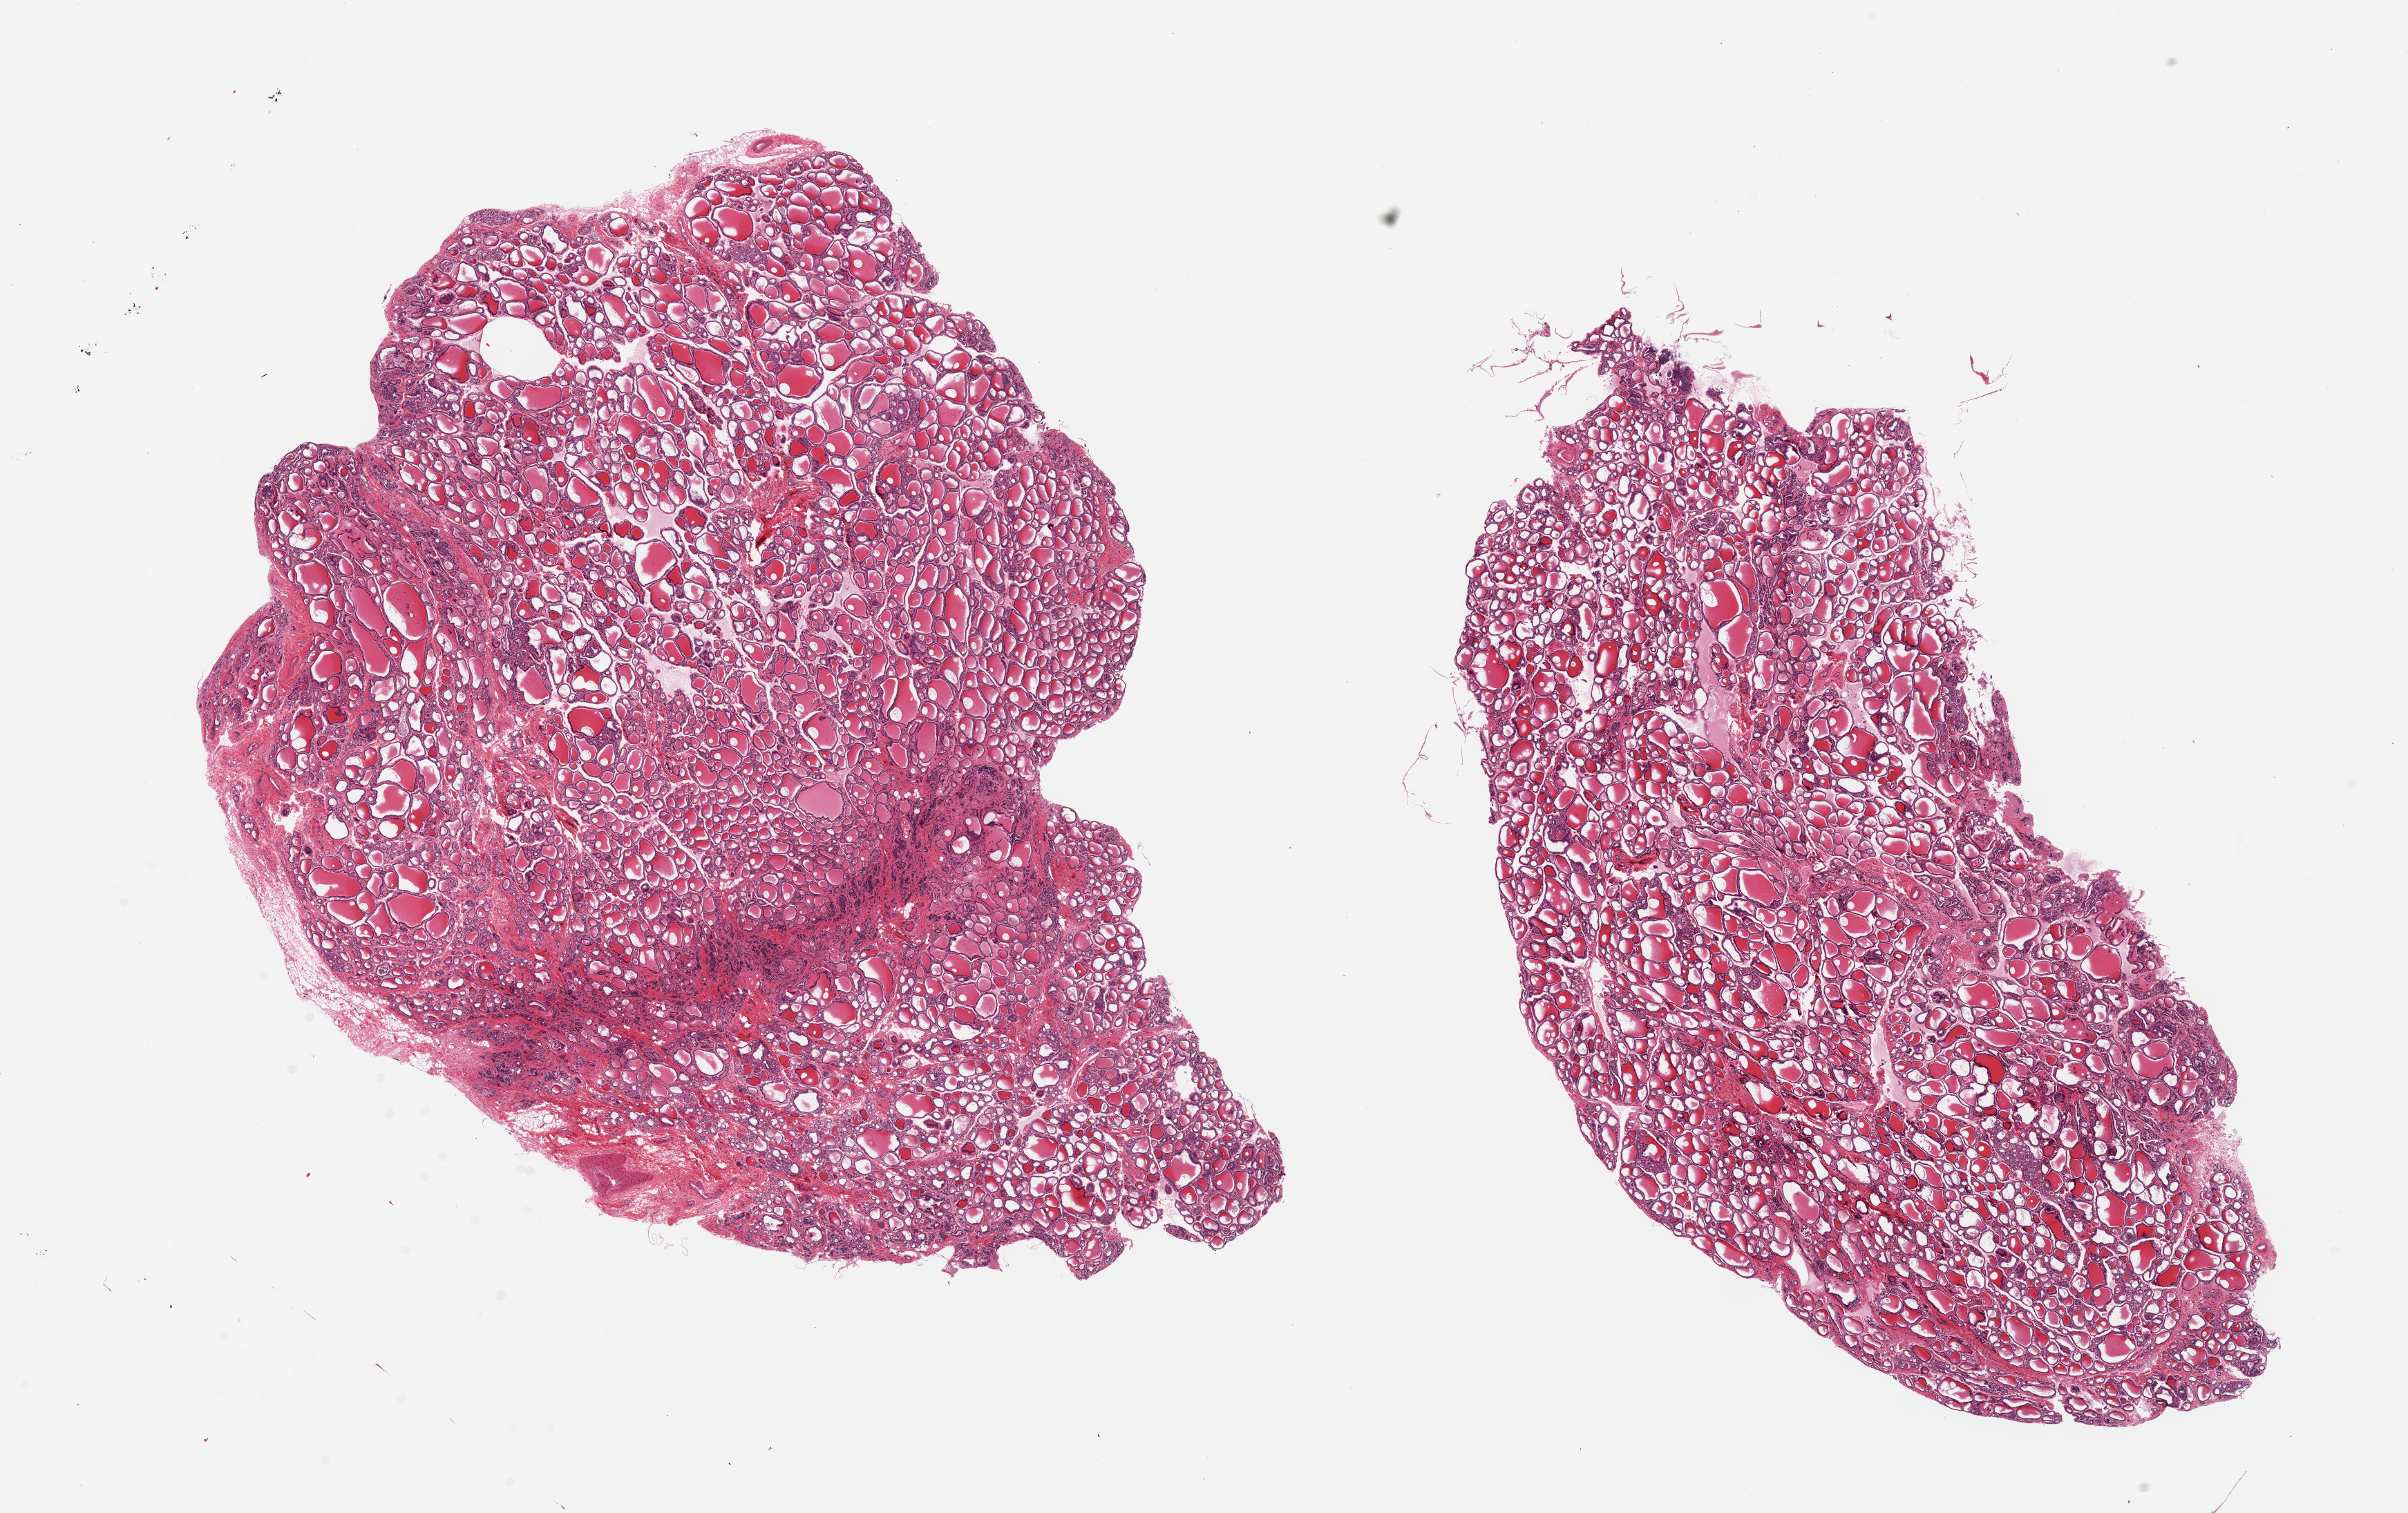
Digitized H&E-stained section, brightfield, shown as a low-resolution overview of the whole scanned area (about 27.6 x 17.3 mm), PAXgene-fixed, paraffin-embedded tissue, target tissue: thyroid, tissue donor sample. Donor: female.
- review note (as recorded): 2 pieces, no abnormalities